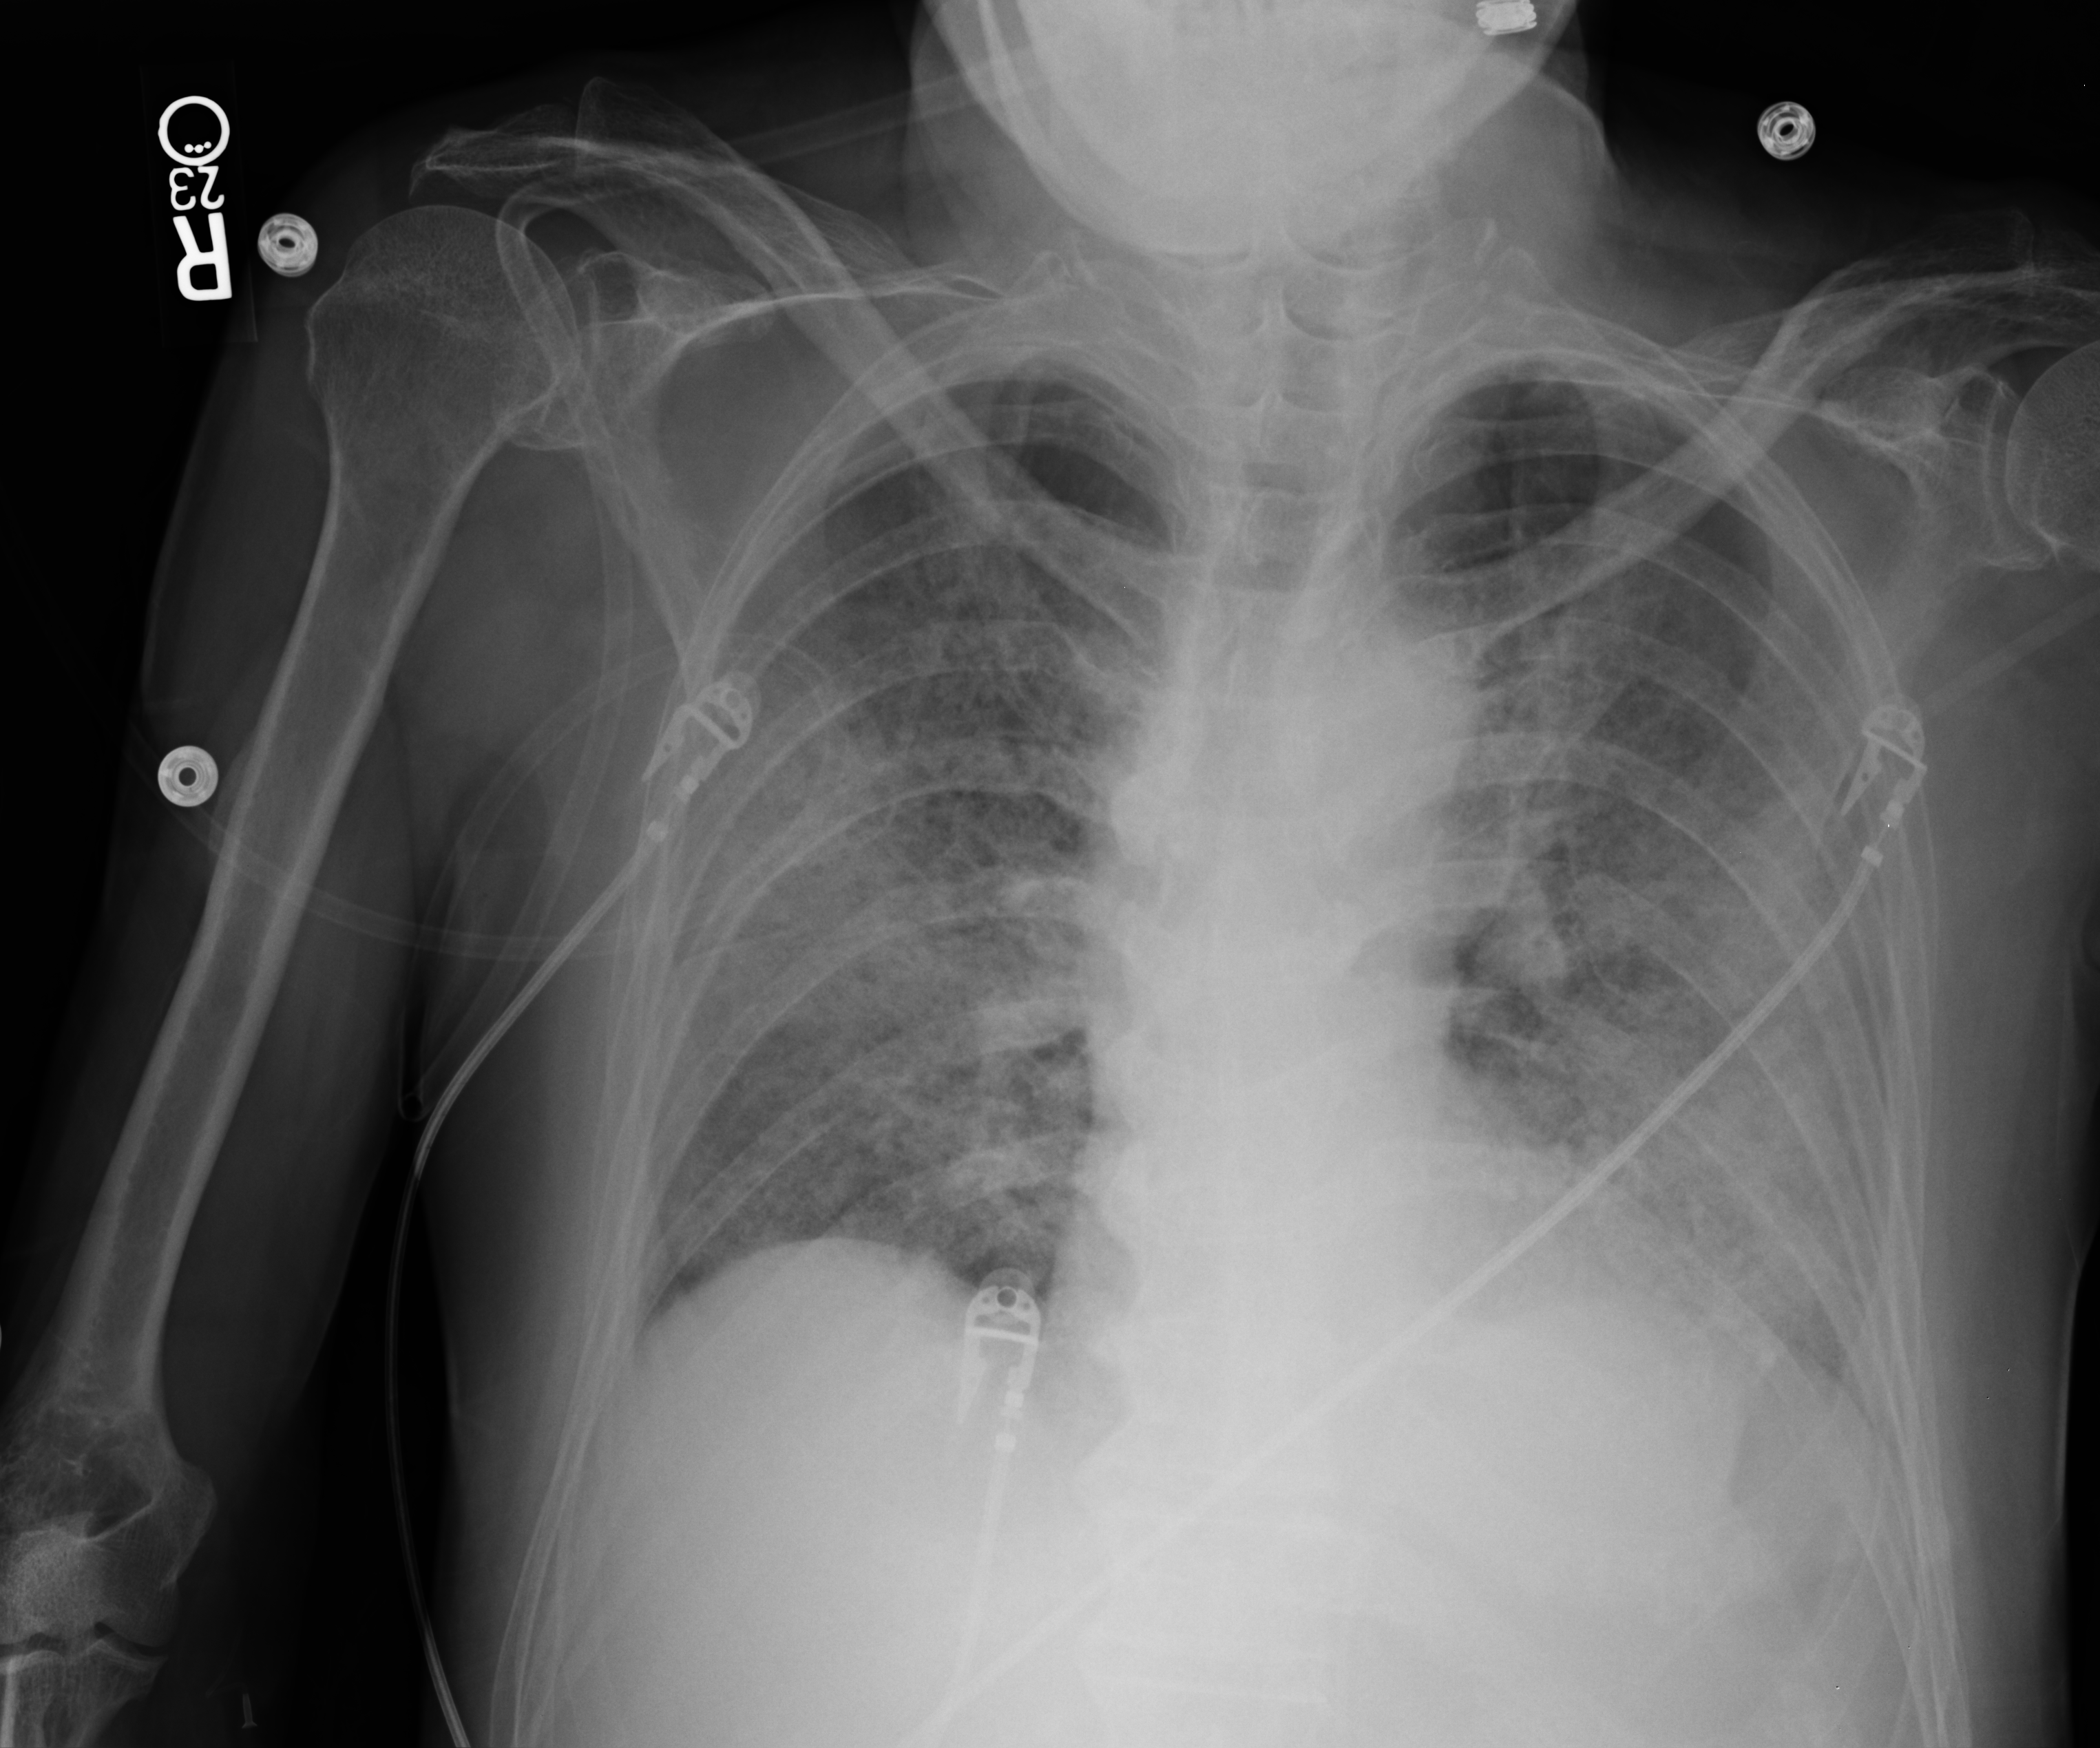
Bedside chest radiograph (computed radiography); anteroposterior (AP) projection. Male patient hospitalised with COVID-19, age 60–74 years.
Hospital-stay facts (about this admission, not read from this image; timing relative to this image not recorded):
- mechanically ventilated during this hospital stay: yes
- smoking status (admission record): current
- admitted to intensive care during this hospital stay: yes